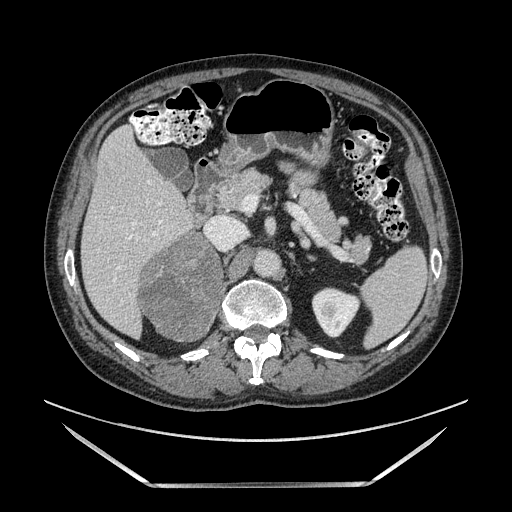
Contrast-enhanced abdominal CT, one axial slice. Position 78 of 185 along the scan axis. Soft-tissue window (W 400 / L 40 HU). 1.25 mm slice thickness. 512 × 512 image matrix. Male patient. From the clinical record (not read from this slice): diagnosis: adrenocortical carcinoma; tumour side: right adrenal; tumour size at pathology: 10.3 cm; Ki-67 index: 20 %; stage (as recorded): 3.
Structures marked on this image (semi-automatically segmented with operator editing):
- mass: box from (x=141, y=235) to (x=220, y=338) px